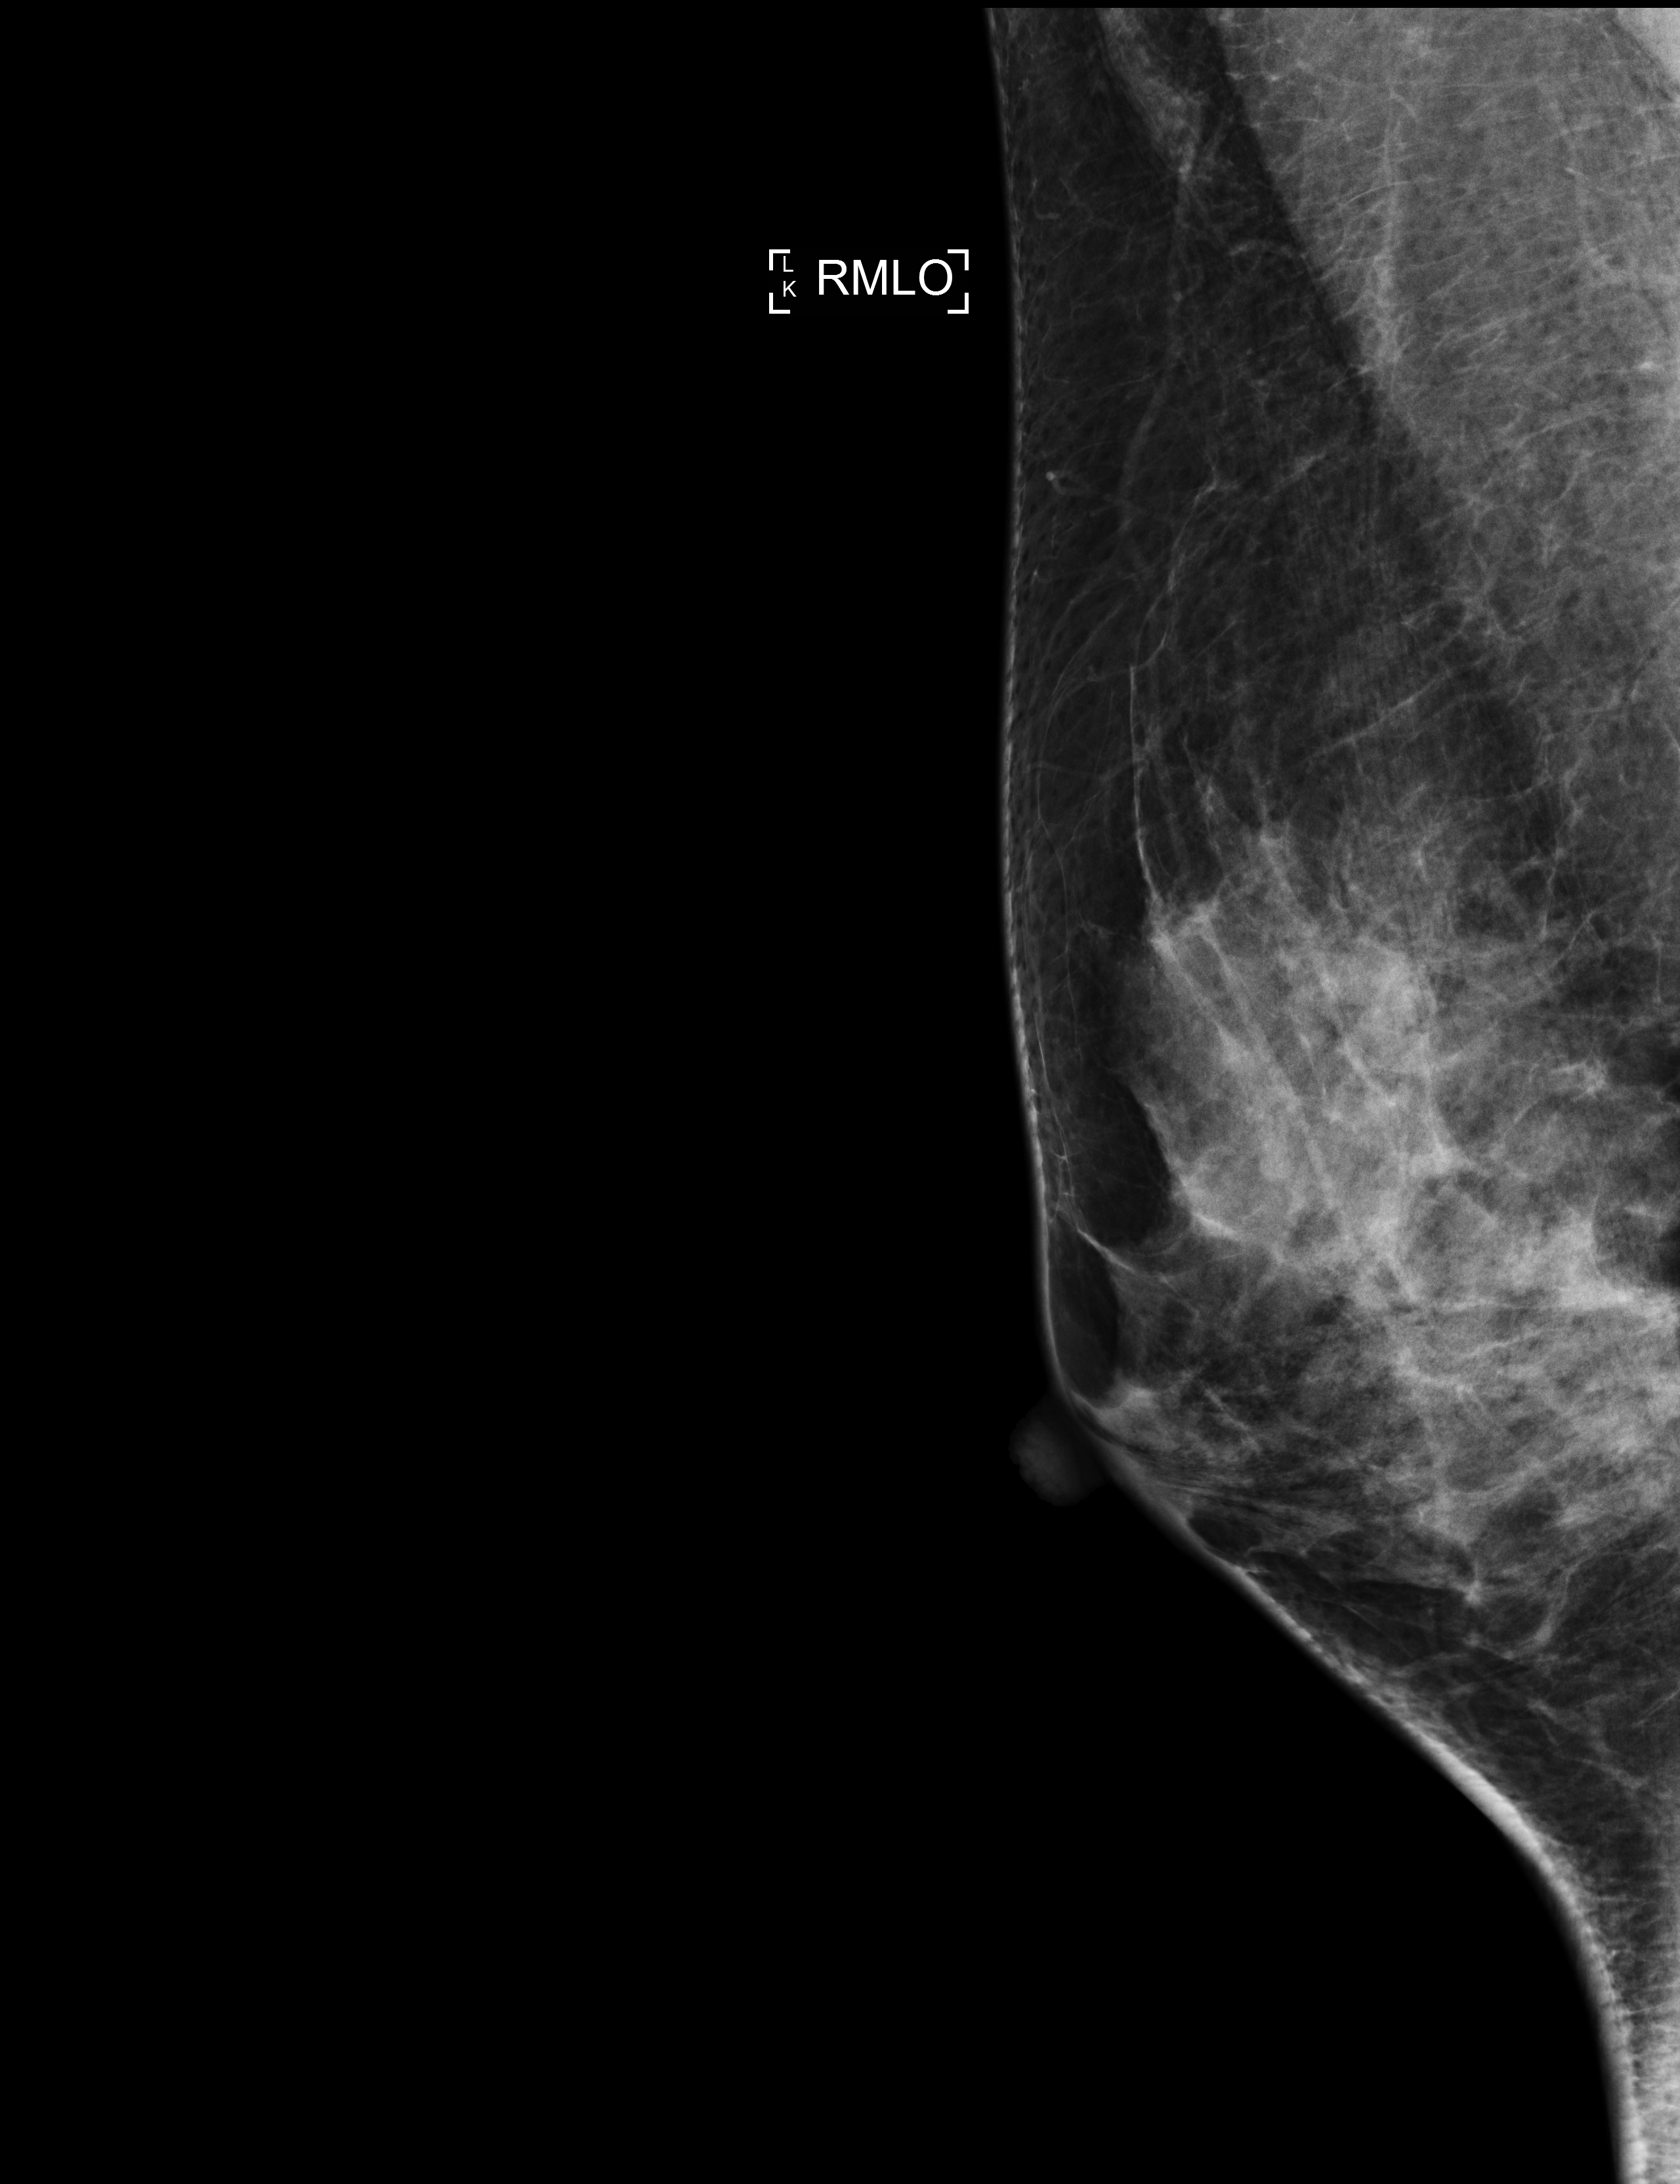
Annual screening mammography examination, compressed breast thickness 56 mm, system: Selenia Dimensions. Patient: female, 44 years.
Image type: full-field digital mammogram. Breast: right. Projection: MLO view.